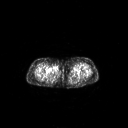
FDG PET of an extremity soft-tissue mass (from a PET/CT study), one axial slice; position 240 of 311 along the scan axis; 3.27 mm slice thickness; 128 × 128 image matrix. Female patient, age 78 years. Case-level facts recorded for this patient, not image findings: histological type: leiomyosarcoma; grade: intermediate; site of the primary tumour: parascapusular.
Structures marked on this image (expert contour drawn on MRI and transferred to this co-registered scan by the dataset authors):
- gross tumour volume including surrounding oedema: bounding box (x1, y1, x2, y2) in pixels: (52, 65, 60, 74)
- gross tumour volume (mass): (53, 65, 59, 72)